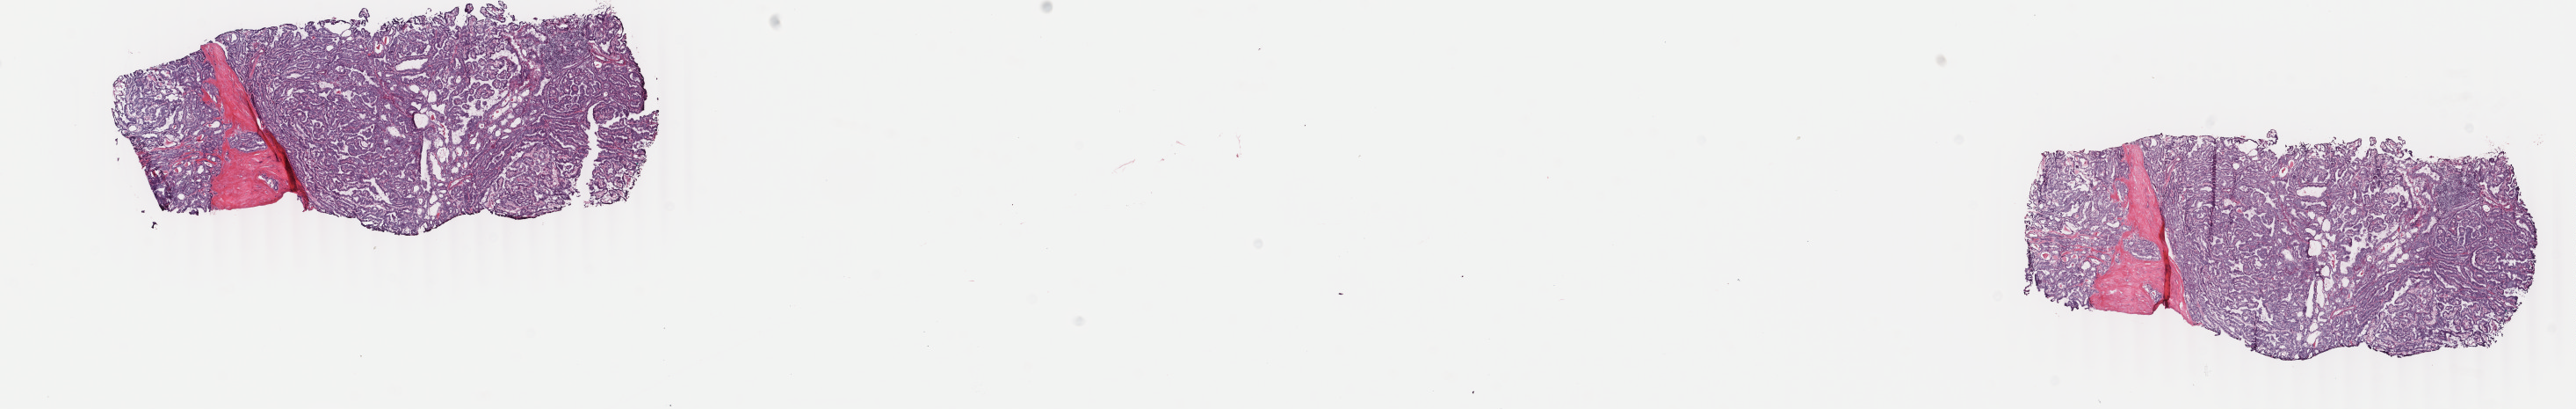
Whole-slide histology image, H&E — a low-resolution overview of the entire scanned area, about 23.3 x 3.7 mm; frozen section from the bottom of the tissue portion; sample: primary tumour, thyroid. Female patient; age at initial diagnosis 65 years. Slide review estimates, as recorded: tumour cells 90%, tumour nuclei 95%, normal cells 0%, stromal cells 10%, necrosis 0%. Inflammatory infiltration, as recorded: lymphocyte infiltration 2%, monocyte infiltration 0%, neutrophil infiltration 0%.
• laterality: right
• lymph nodes positive (case pathology): 5 of 7 examined
• pathologic diagnosis: Papillary adenocarcinoma, NOS (thyroid gland)
• AJCC pathologic stage: III (6th edition)